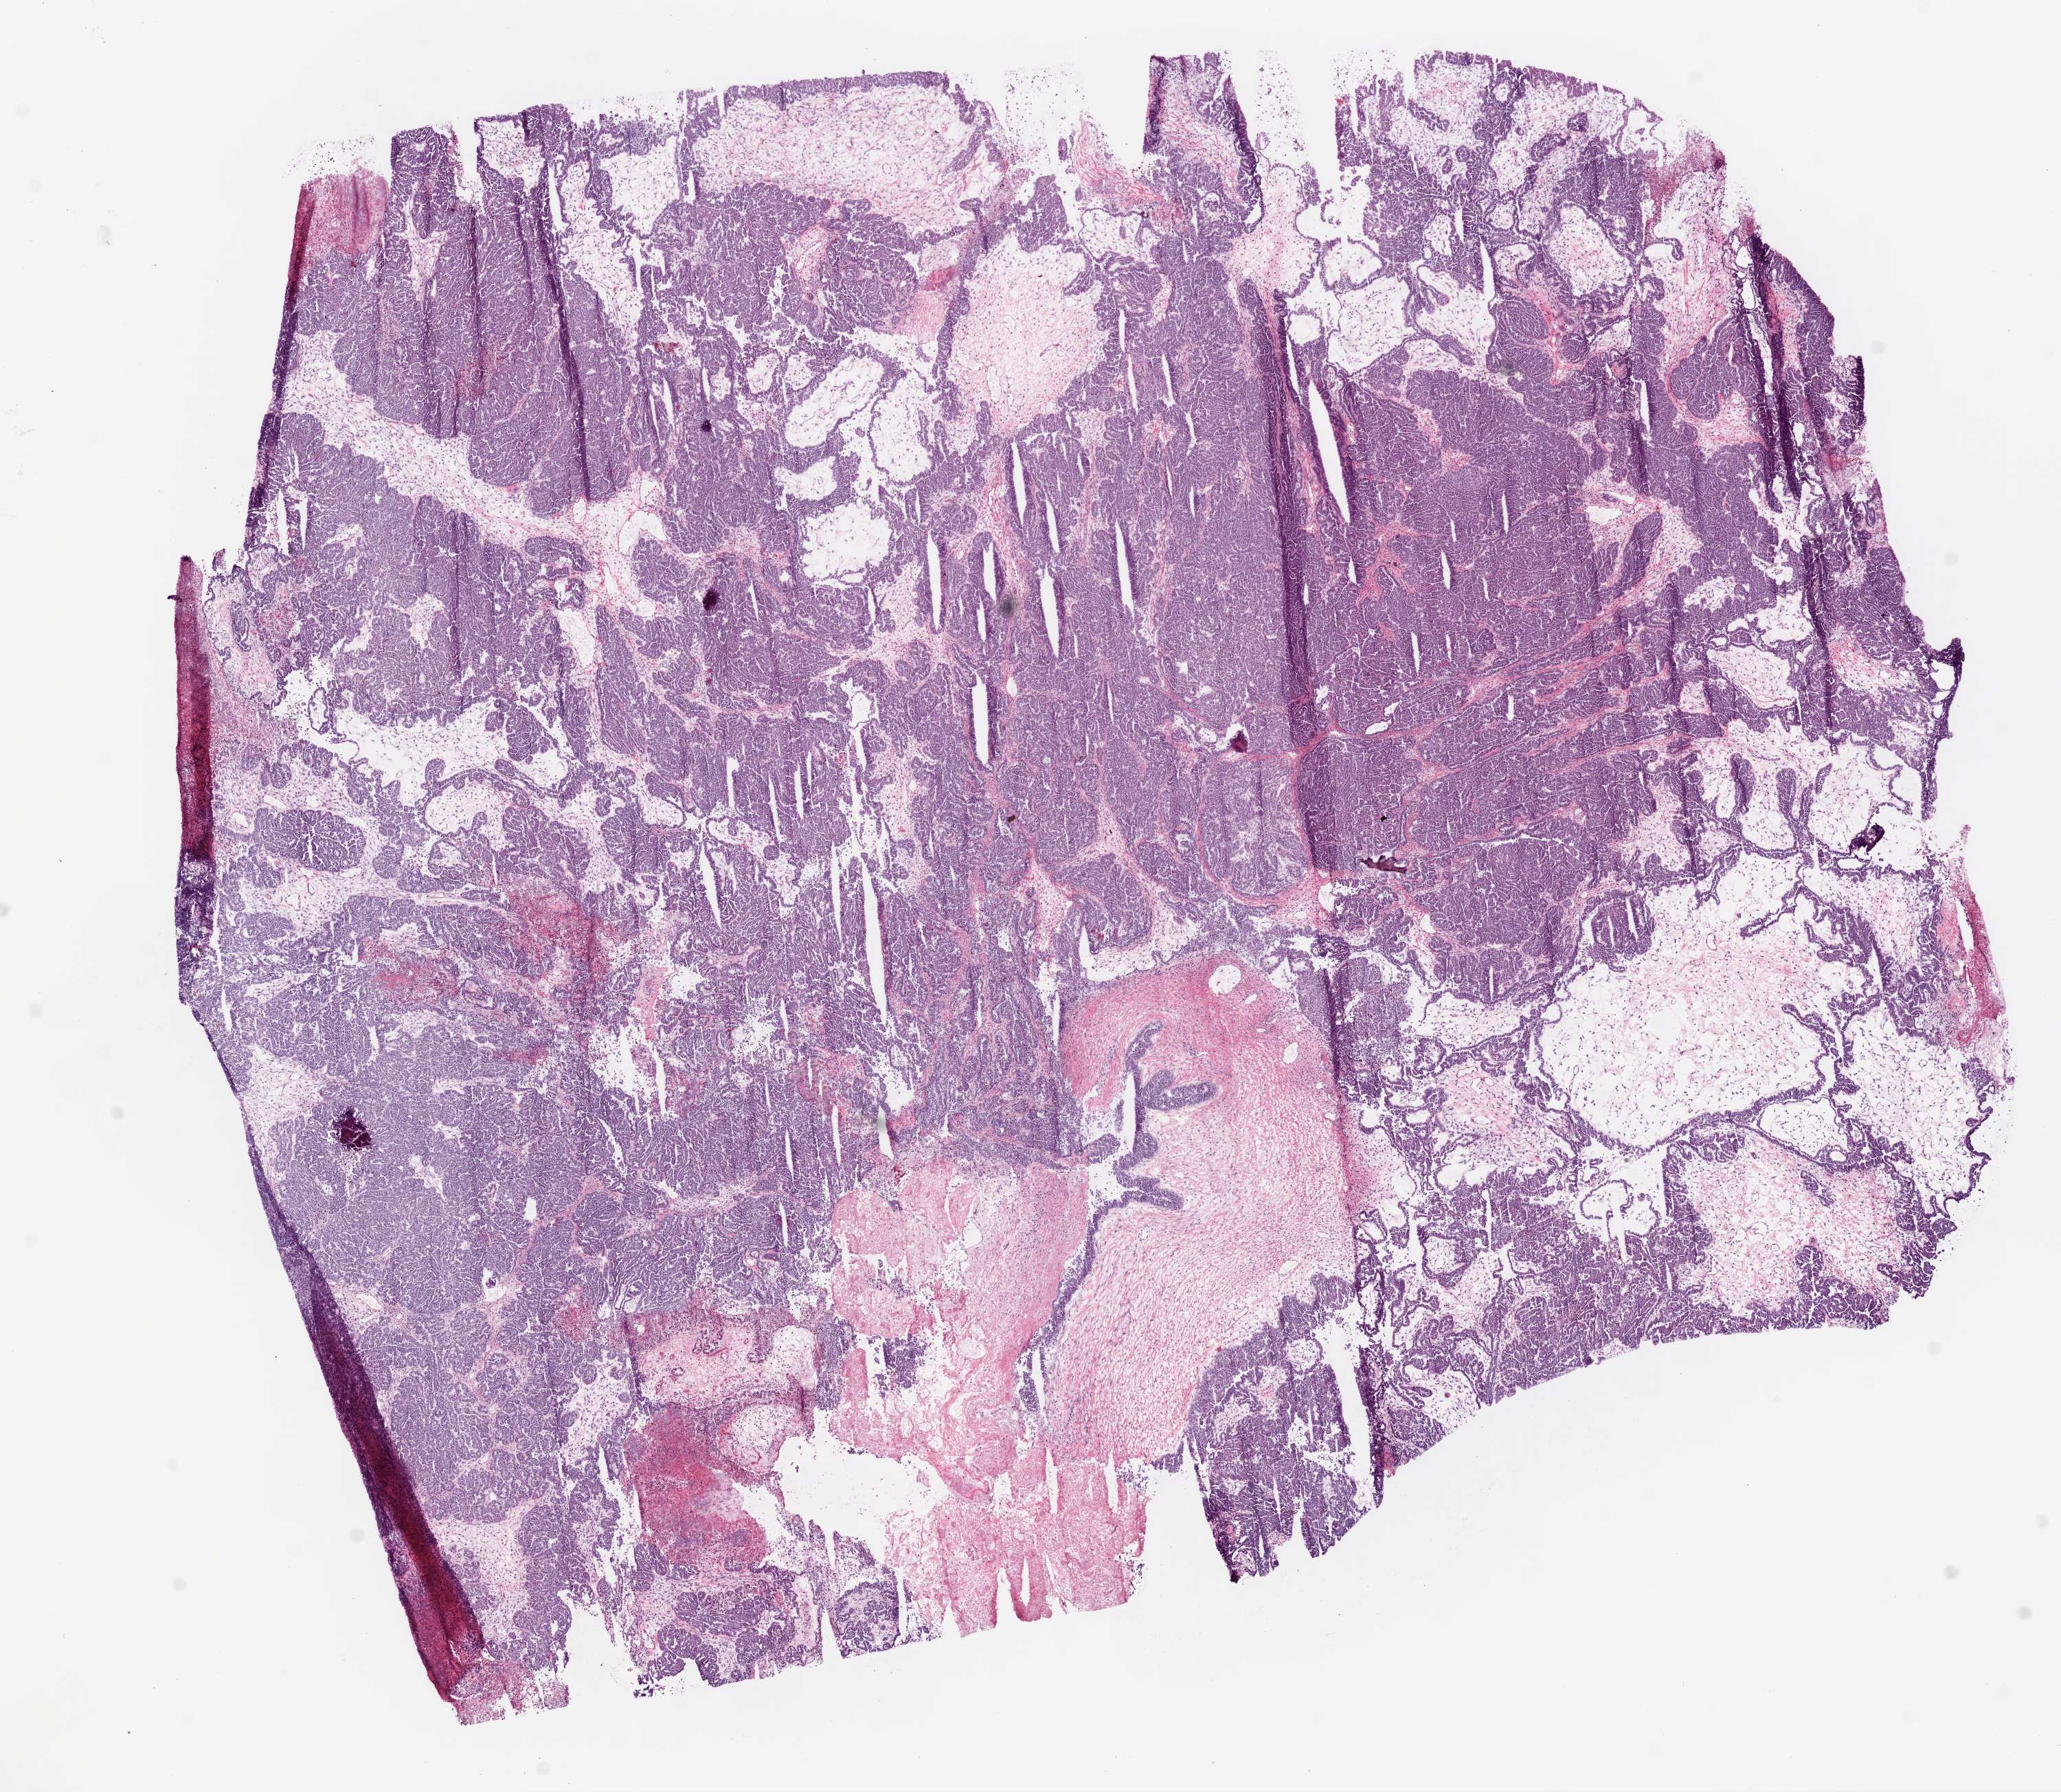
H&E-stained whole-slide image, low-resolution overview of the scanned area, about 12.0 x 10.5 mm (acquisition: 20x scan), frozen section from the bottom of the tissue portion, sample: primary tumour, ovary. Female patient; age at initial diagnosis 39 years. Histologic grade: G3 (poorly differentiated). Slide review estimates, as recorded: tumour cells 82%, tumour nuclei 90%, normal cells 0%, stromal cells 10%, necrosis 8%.
Laterality: bilateral. FIGO stage: IIIC. Diagnosis: Serous cystadenocarcinoma, NOS.